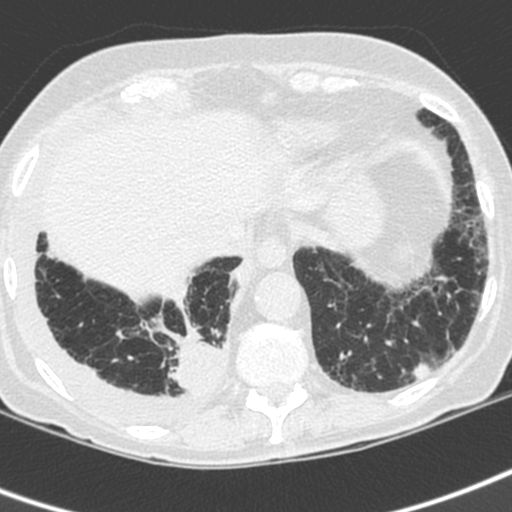
Low-dose screening chest CT, axial slice; first (baseline) screen; lung window (W 1500 / L -600 HU); 1.3 mm slice thickness; standard (soft-tissue) reconstruction kernel (C); 120 kVp; slice 154 of 192 in the series; 512 × 512 image matrix. Female participant, aged 73 years at enrolment. Current smoker at enrolment.
Expert reader's lesion annotation, bounding box [x1, y1, x2, y2] px = [160, 326, 235, 406]. Reader record for this screening exam (exam-level; its link to the box is not recorded): non-calcified nodule or mass ≥4 mm, right lower lobe, 35 × 30 mm, spiculated (stellate) margins, soft tissue attenuation. Official screen result: positive, change unspecified: nodule(s) >= 4 mm or enlarging nodule(s), mass(es), or other non-specific abnormalities suspicious for lung cancer.